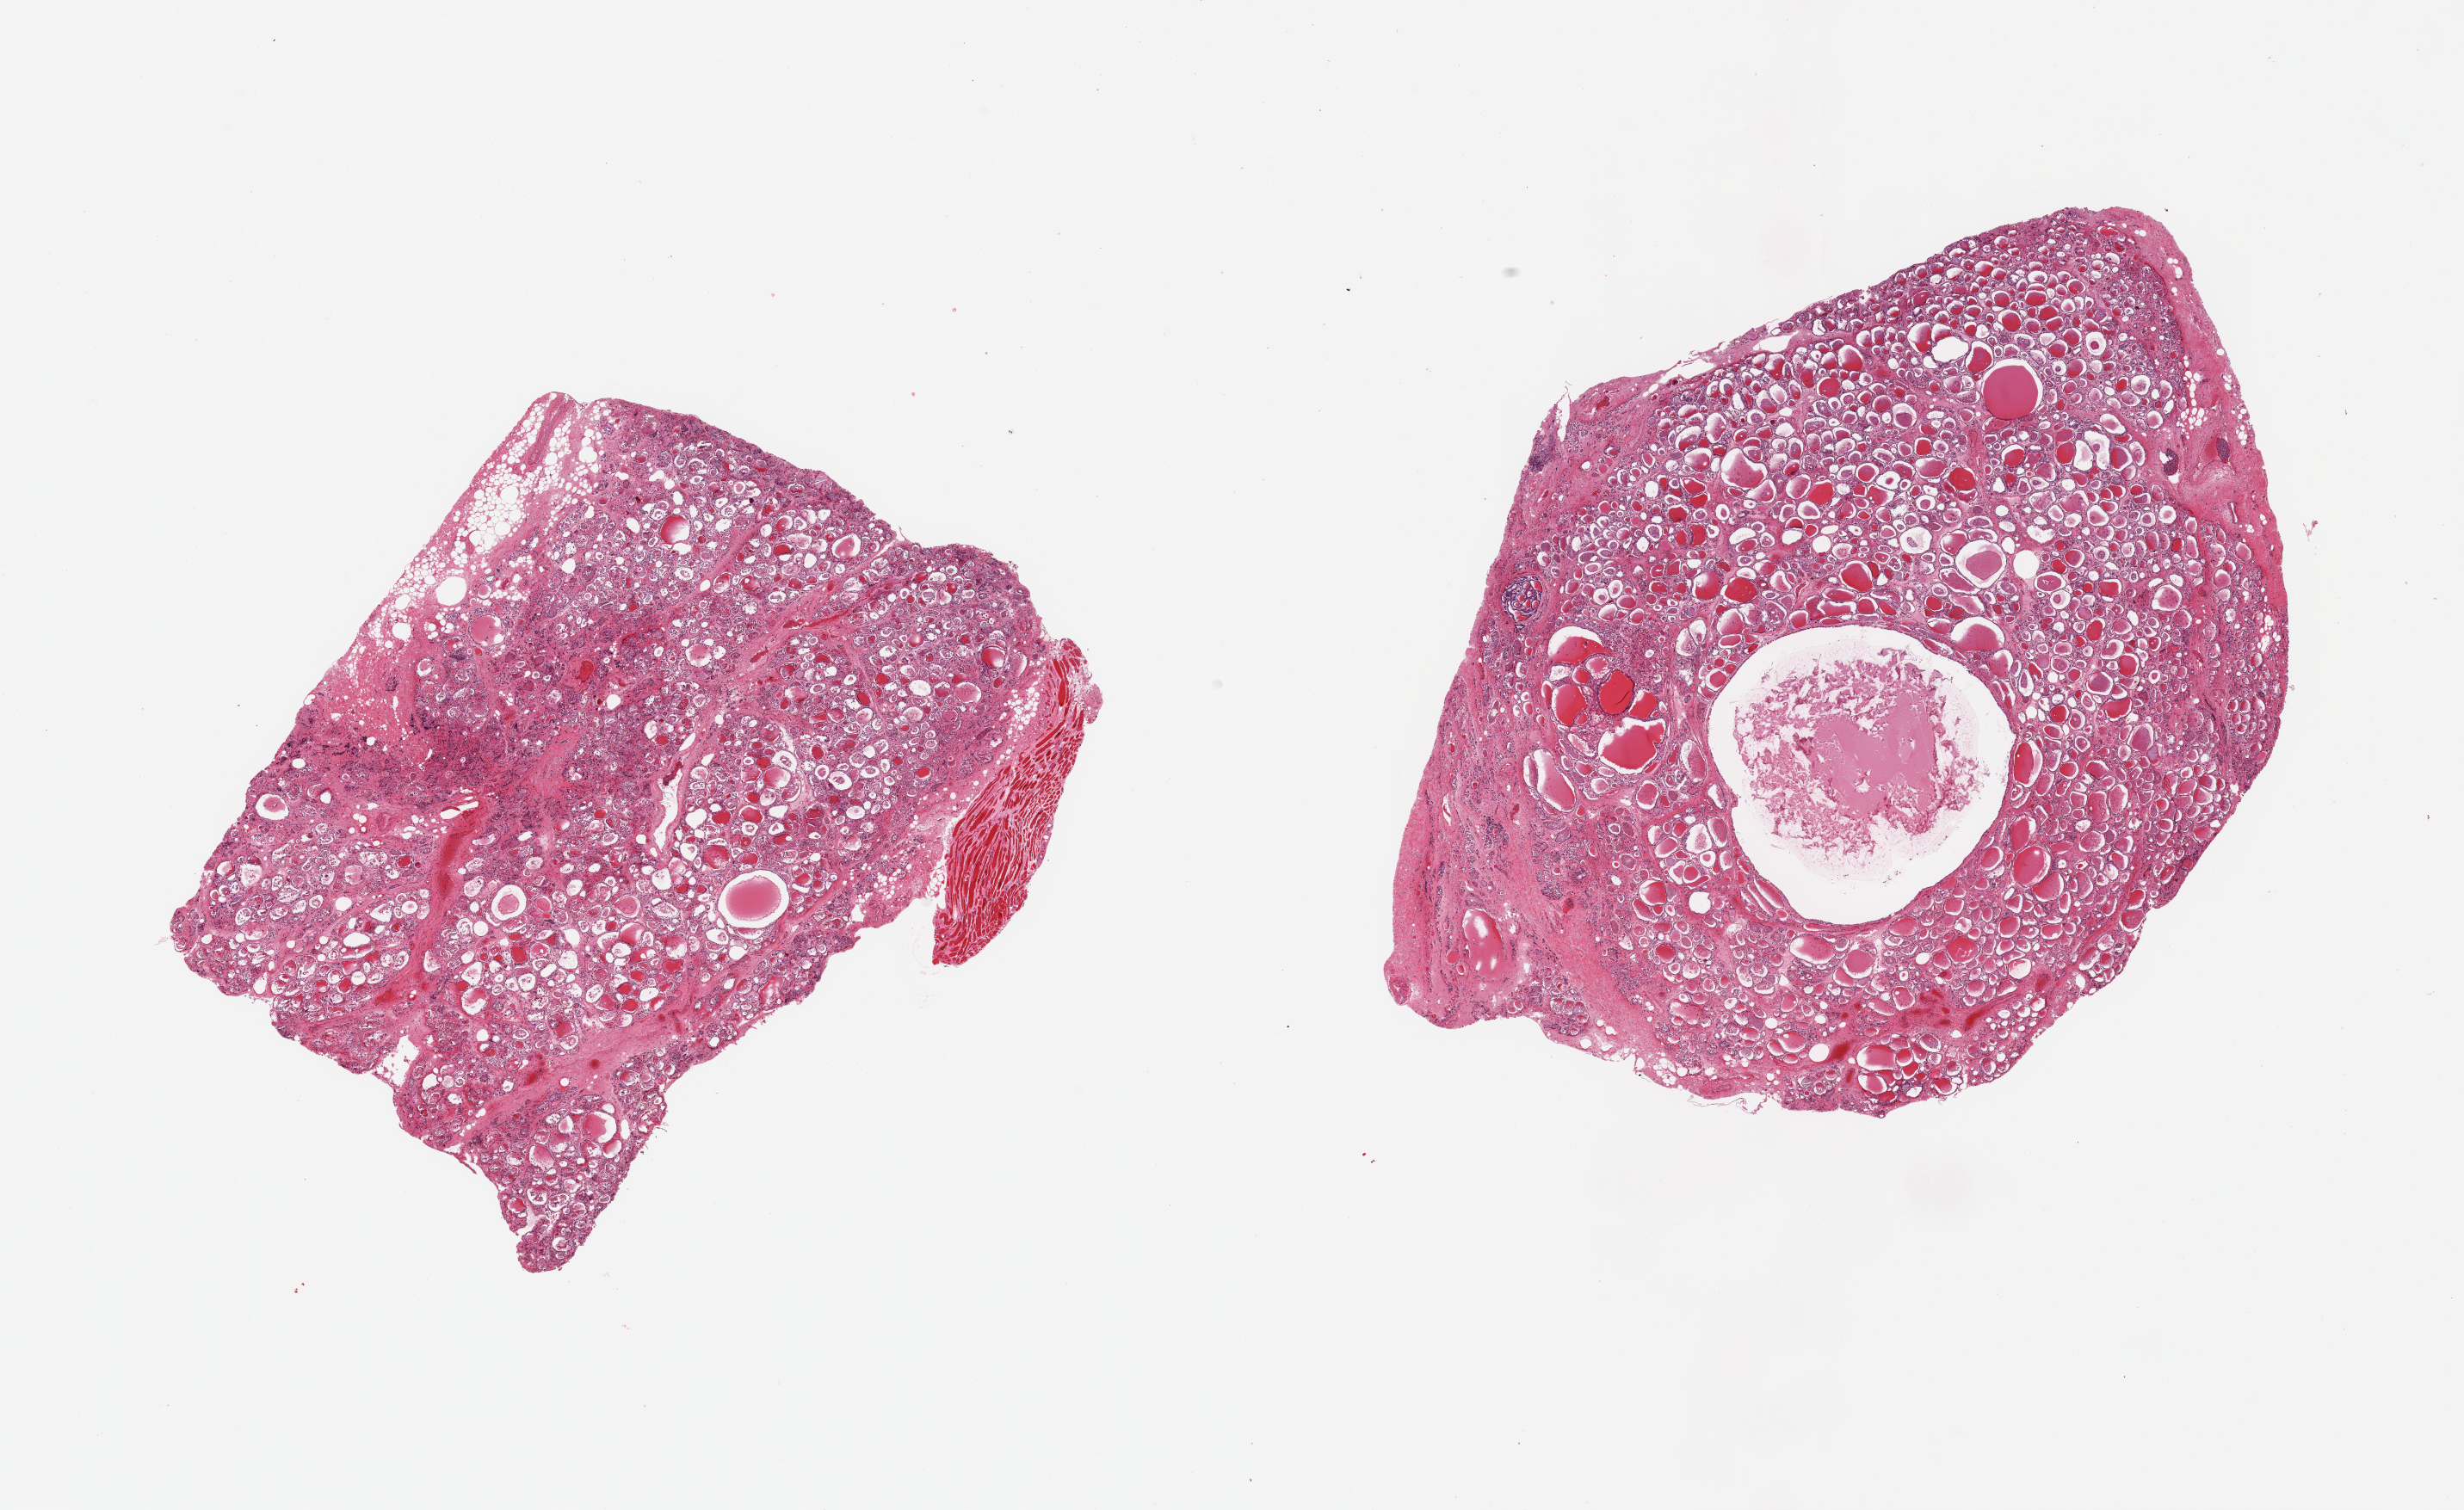
Digitized hematoxylin and eosin (H&E)-stained section, a low-resolution overview of the entire scanned area, about 22.6 x 13.9 mm (slide scanned at 20x); PAXgene-fixed, paraffin-embedded tissue; target tissue: thyroid; donor tissue sample. Female donor.
* pathologist's review note for this sample: 2 pieces, regressive changes, ~2.5mm colloid cyst